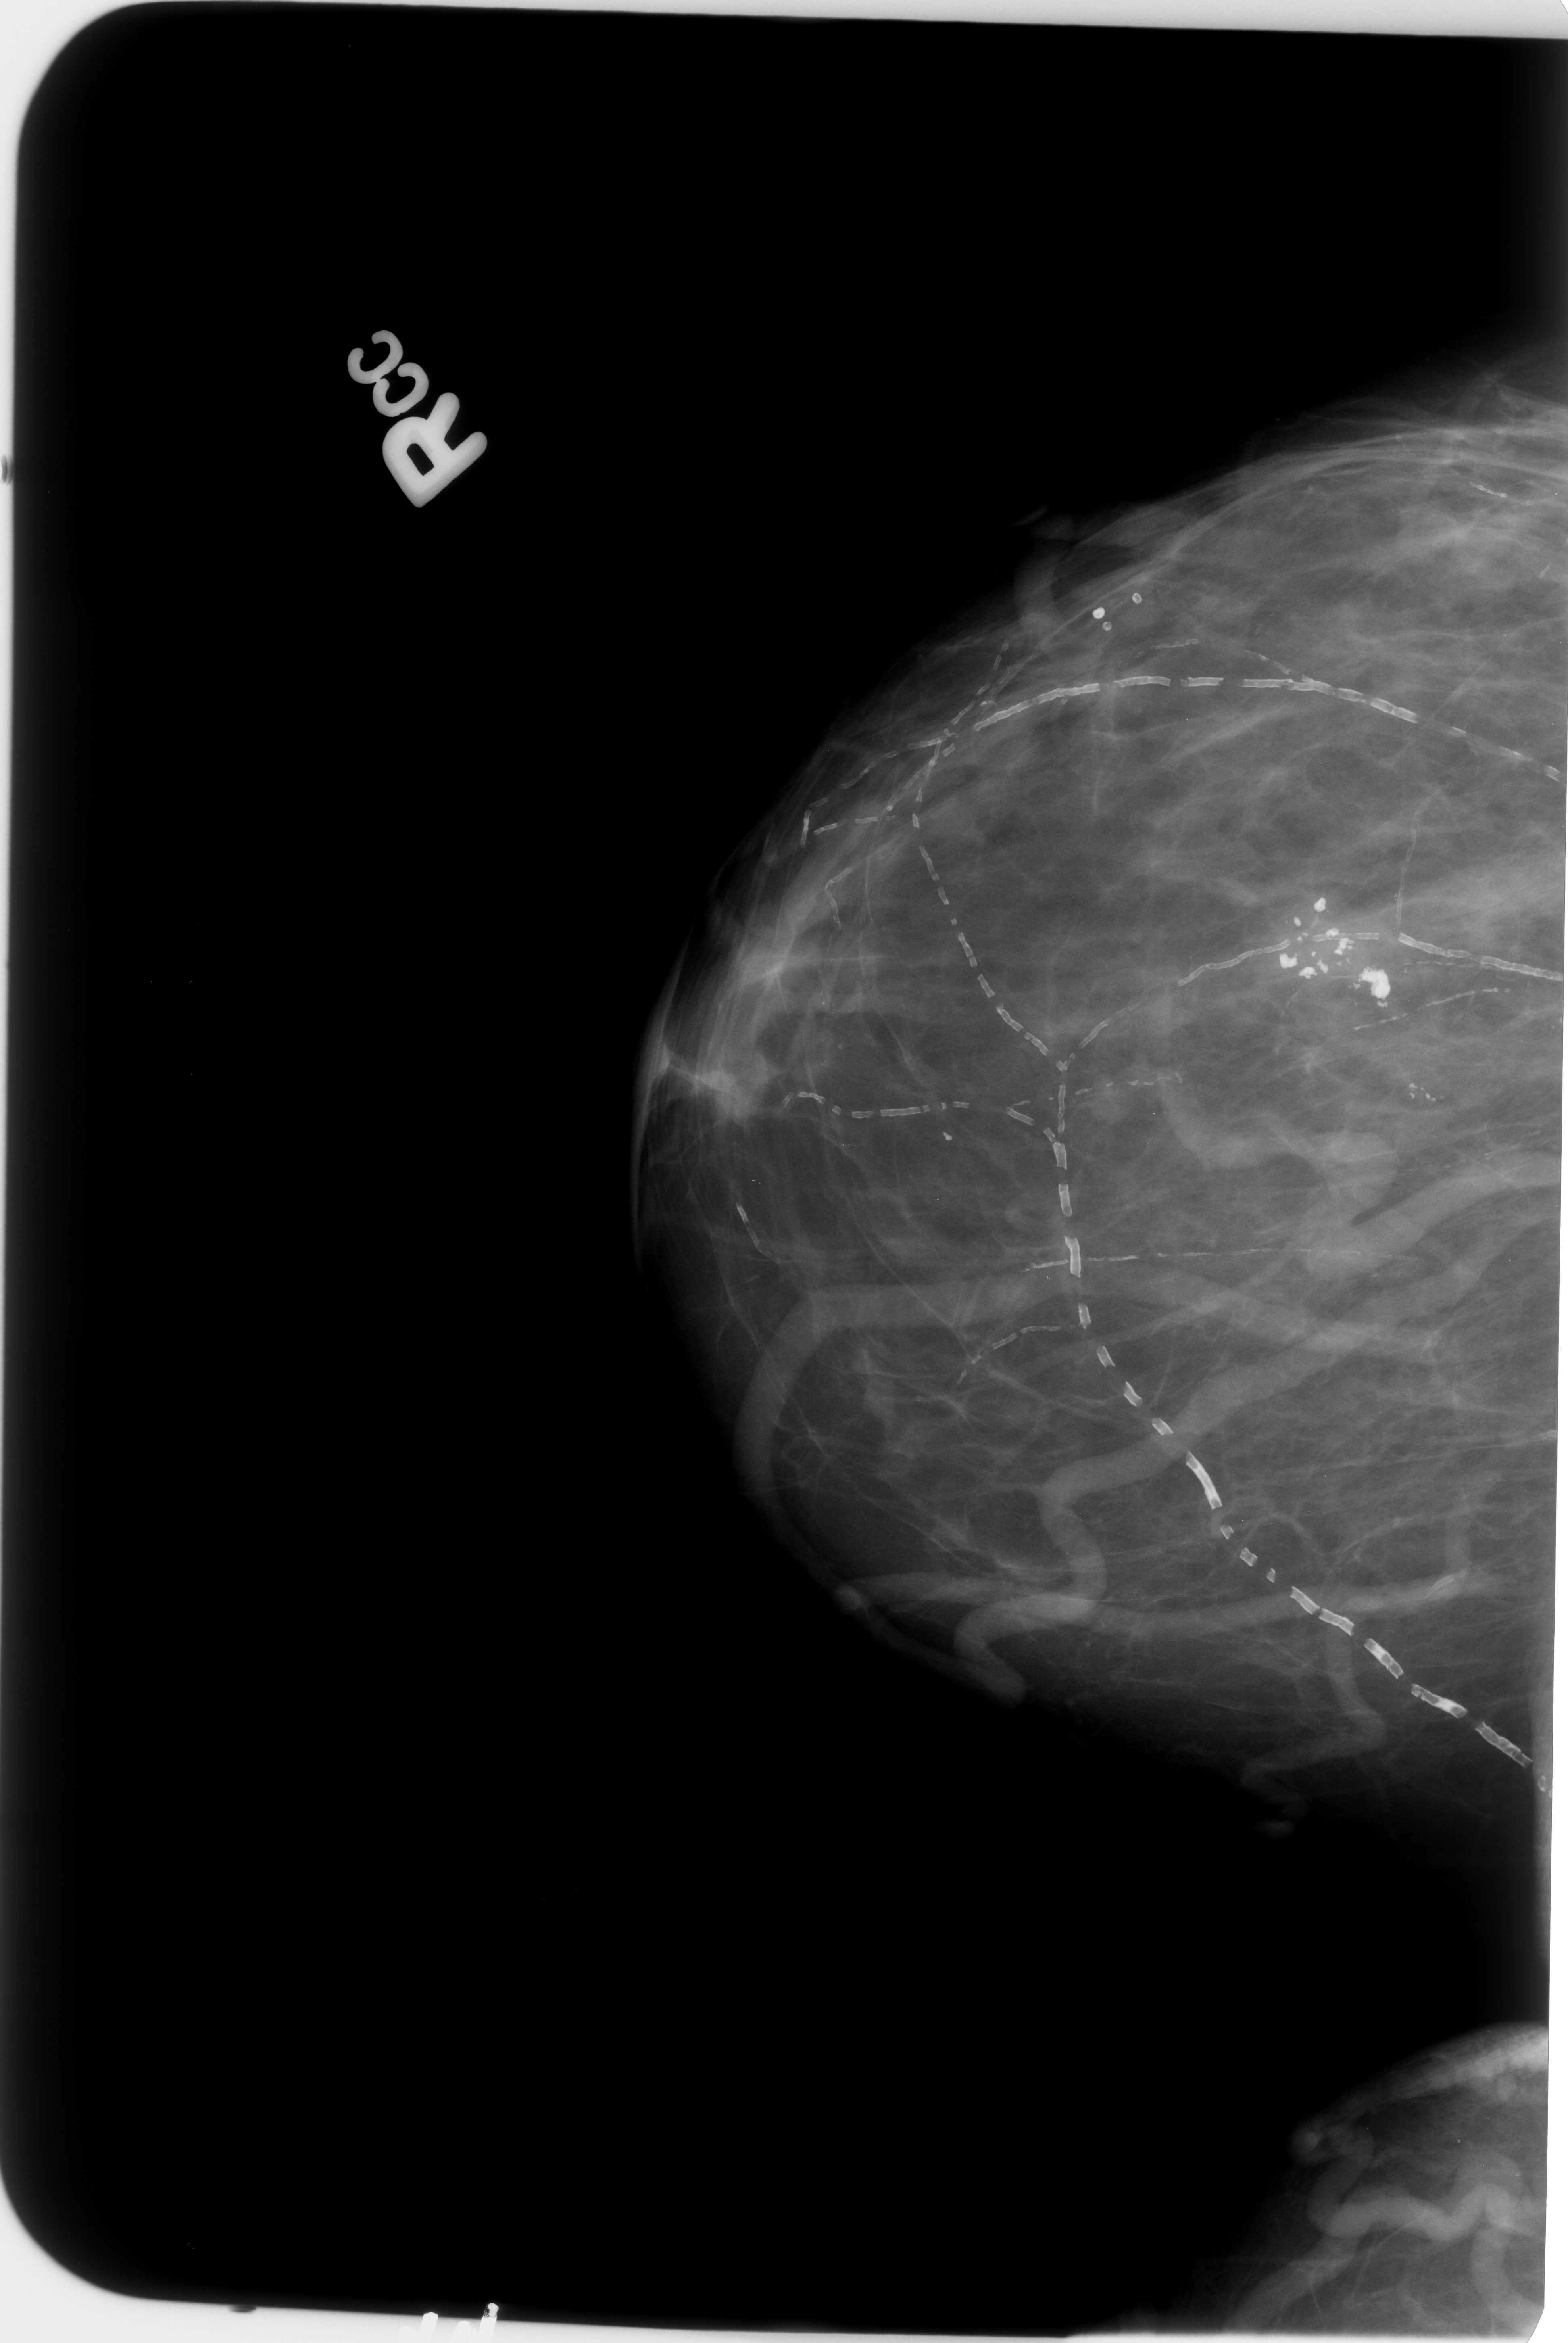
Scanned film-screen mammogram; right breast; CC view; 1568 × 2343 image matrix.
Expert-marked regions of interest on this image (one box per marked abnormality):
- calcifications, morphology coarse / pleomorphic, distribution clustered; BI-RADS assessment category 2; pathology (as recorded): benign: box from (x=1242, y=861) to (x=1382, y=1005) px